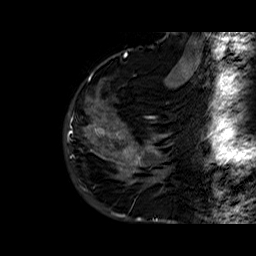
Breast MRI (dynamic contrast-enhanced), one sagittal slice; position 14 of 60 along the scan axis; dynamic contrast-enhanced series, time point 2 of 6 at this slice position (early post-contrast); 1.5 T; TE 6.4 ms, TR 32.8 ms; 4 mm slice thickness; 256 × 256 image matrix, field of view 200 × 200 mm. Female patient. Case-level facts recorded for this patient, not image findings: setting: breast cancer imaged before/during neoadjuvant chemotherapy; receptor status: HR-positive, HER2-negative.
Annotated regions visible in this slice (semi-automatically segmented with operator editing):
- analysis volume of interest (the breast-tissue region the enhancement analysis was run in; not a lesion): box from (x=86, y=77) to (x=163, y=177) px
- tumour enhancement mask (voxels above the 100 % enhancement threshold inside the analysis volume of interest): (x=89, y=77)–(x=141, y=164)